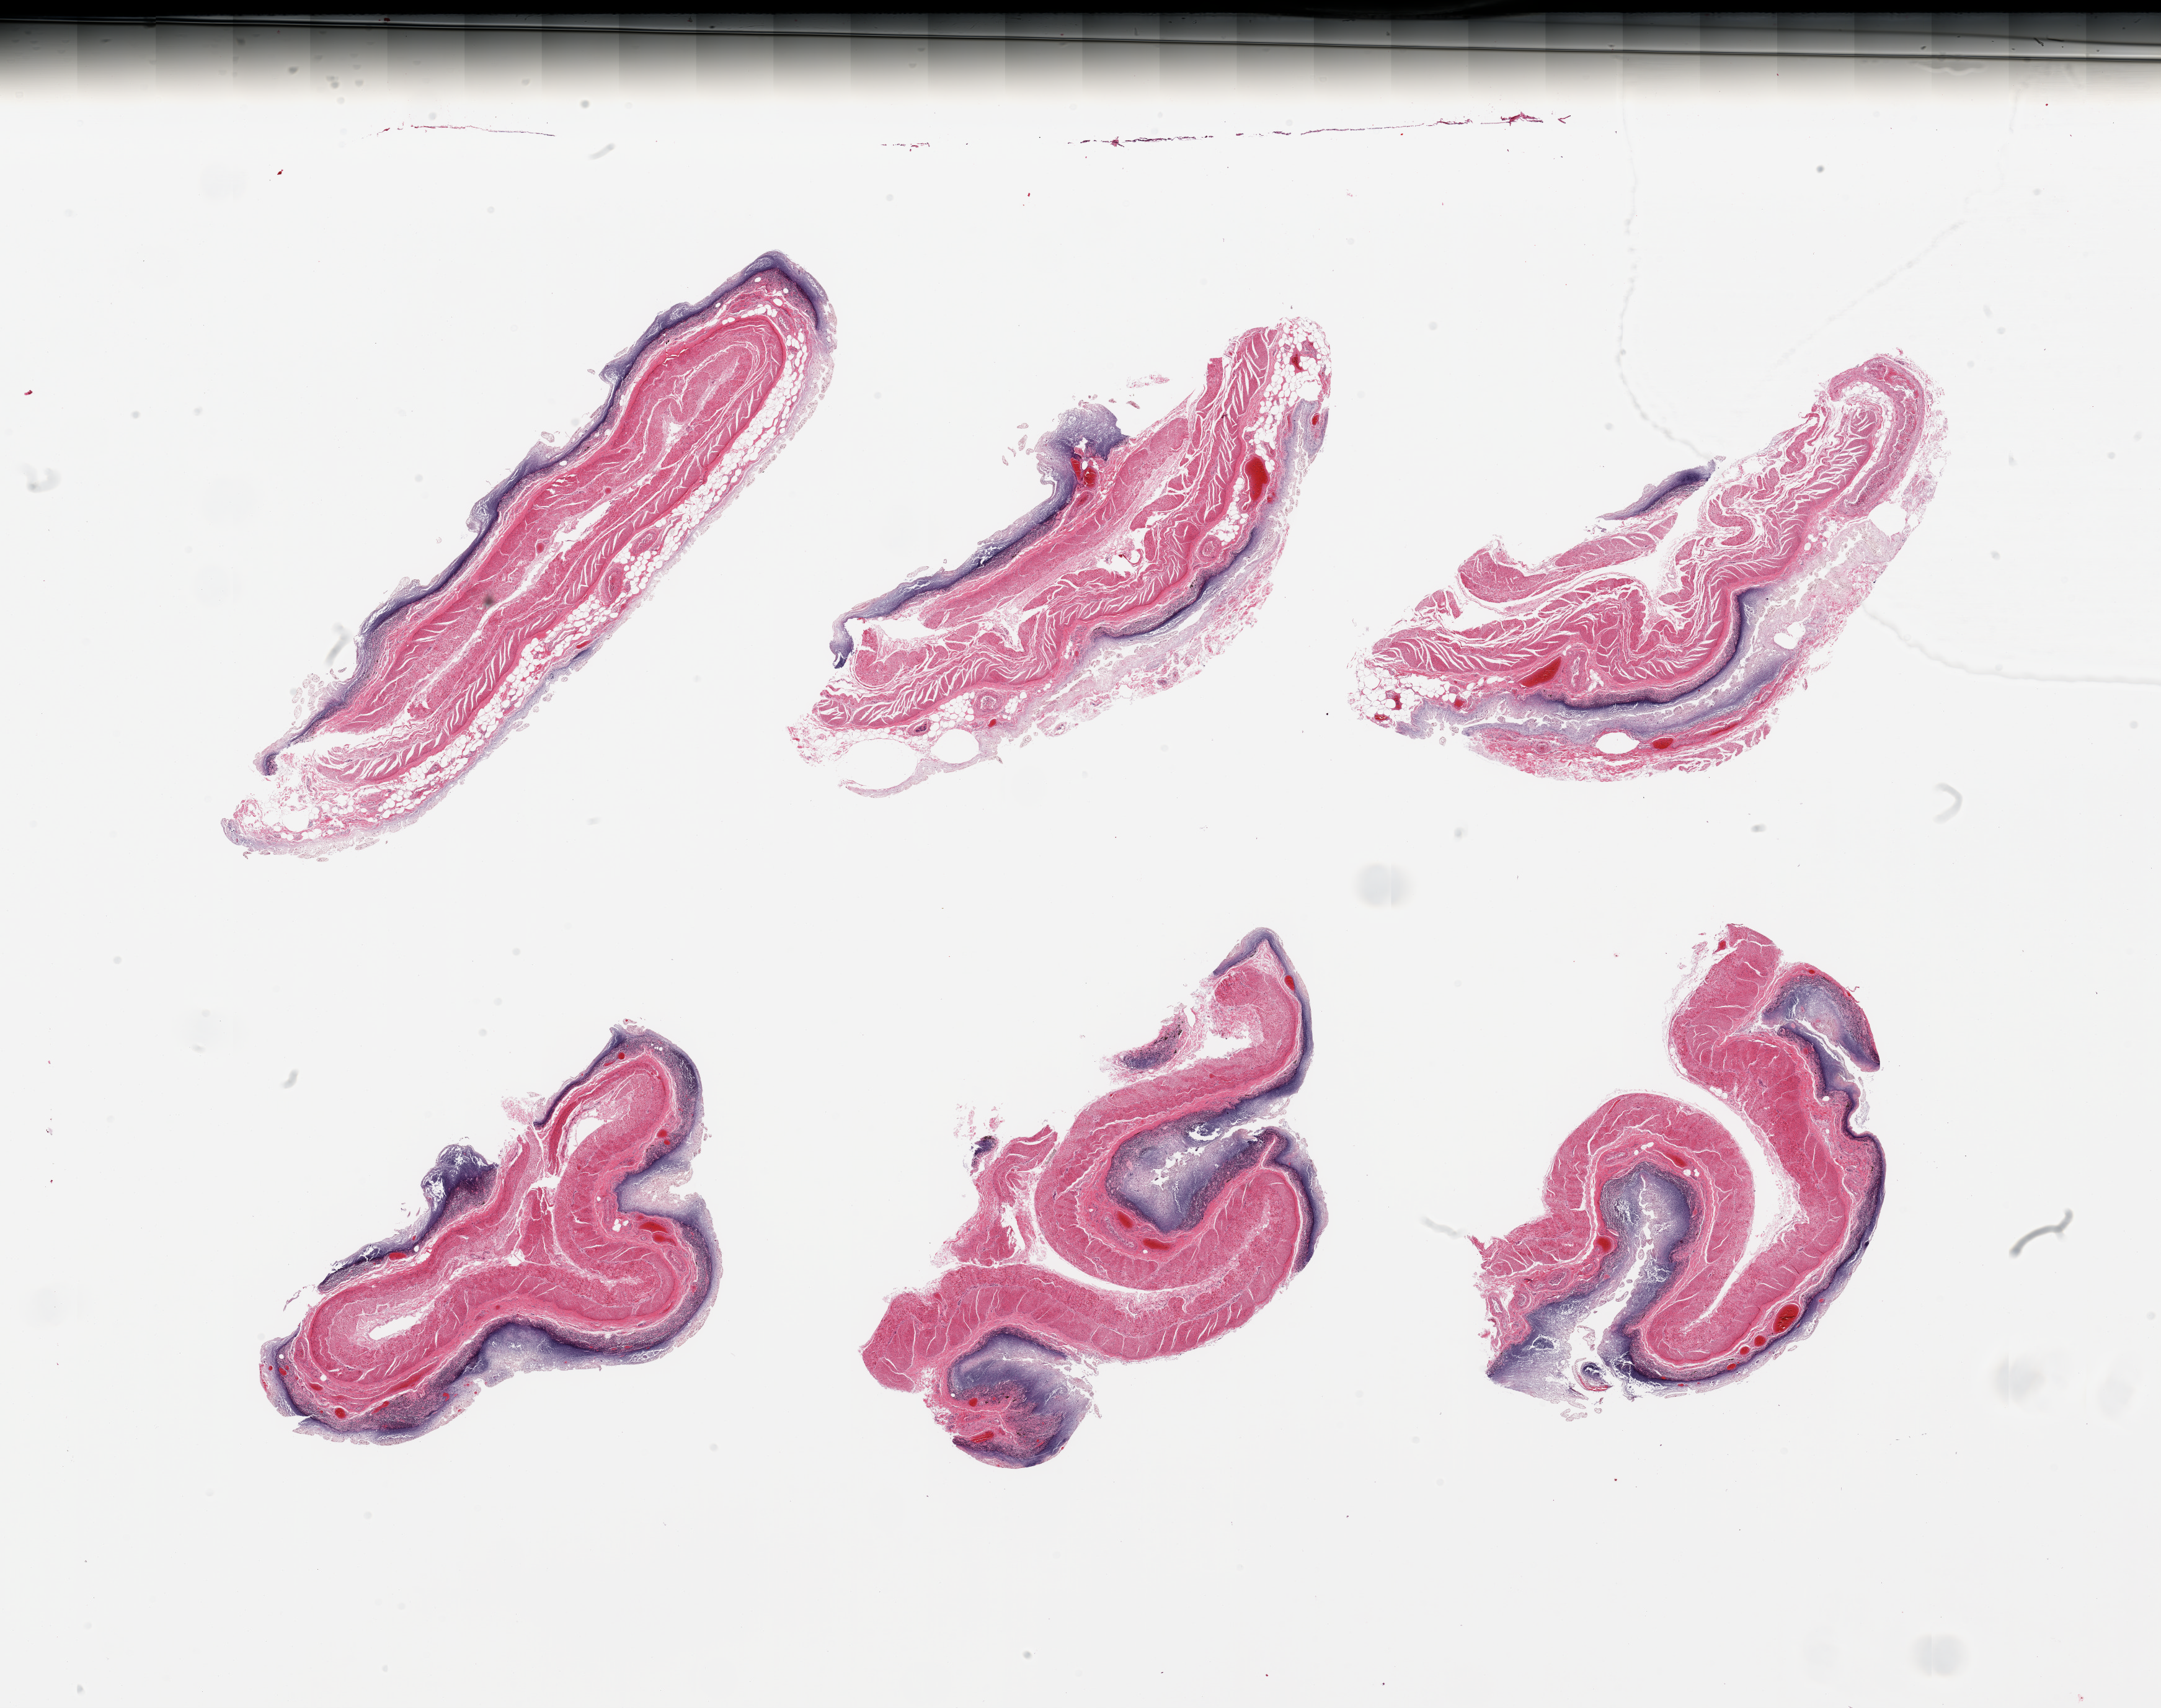
Digitized haematoxylin and eosin-stained section, low-resolution overview of the scanned area, about 27.6 x 21.8 mm (slide scanned at 20x); PAXgene-fixed, paraffin-embedded tissue; target tissue: ileum; donor tissue sample.
Pathologist's review note for this sample: 6 pieces, mucosa completely autolyzed; correct target, insufficient lymphoid tissue to warrant analysis.